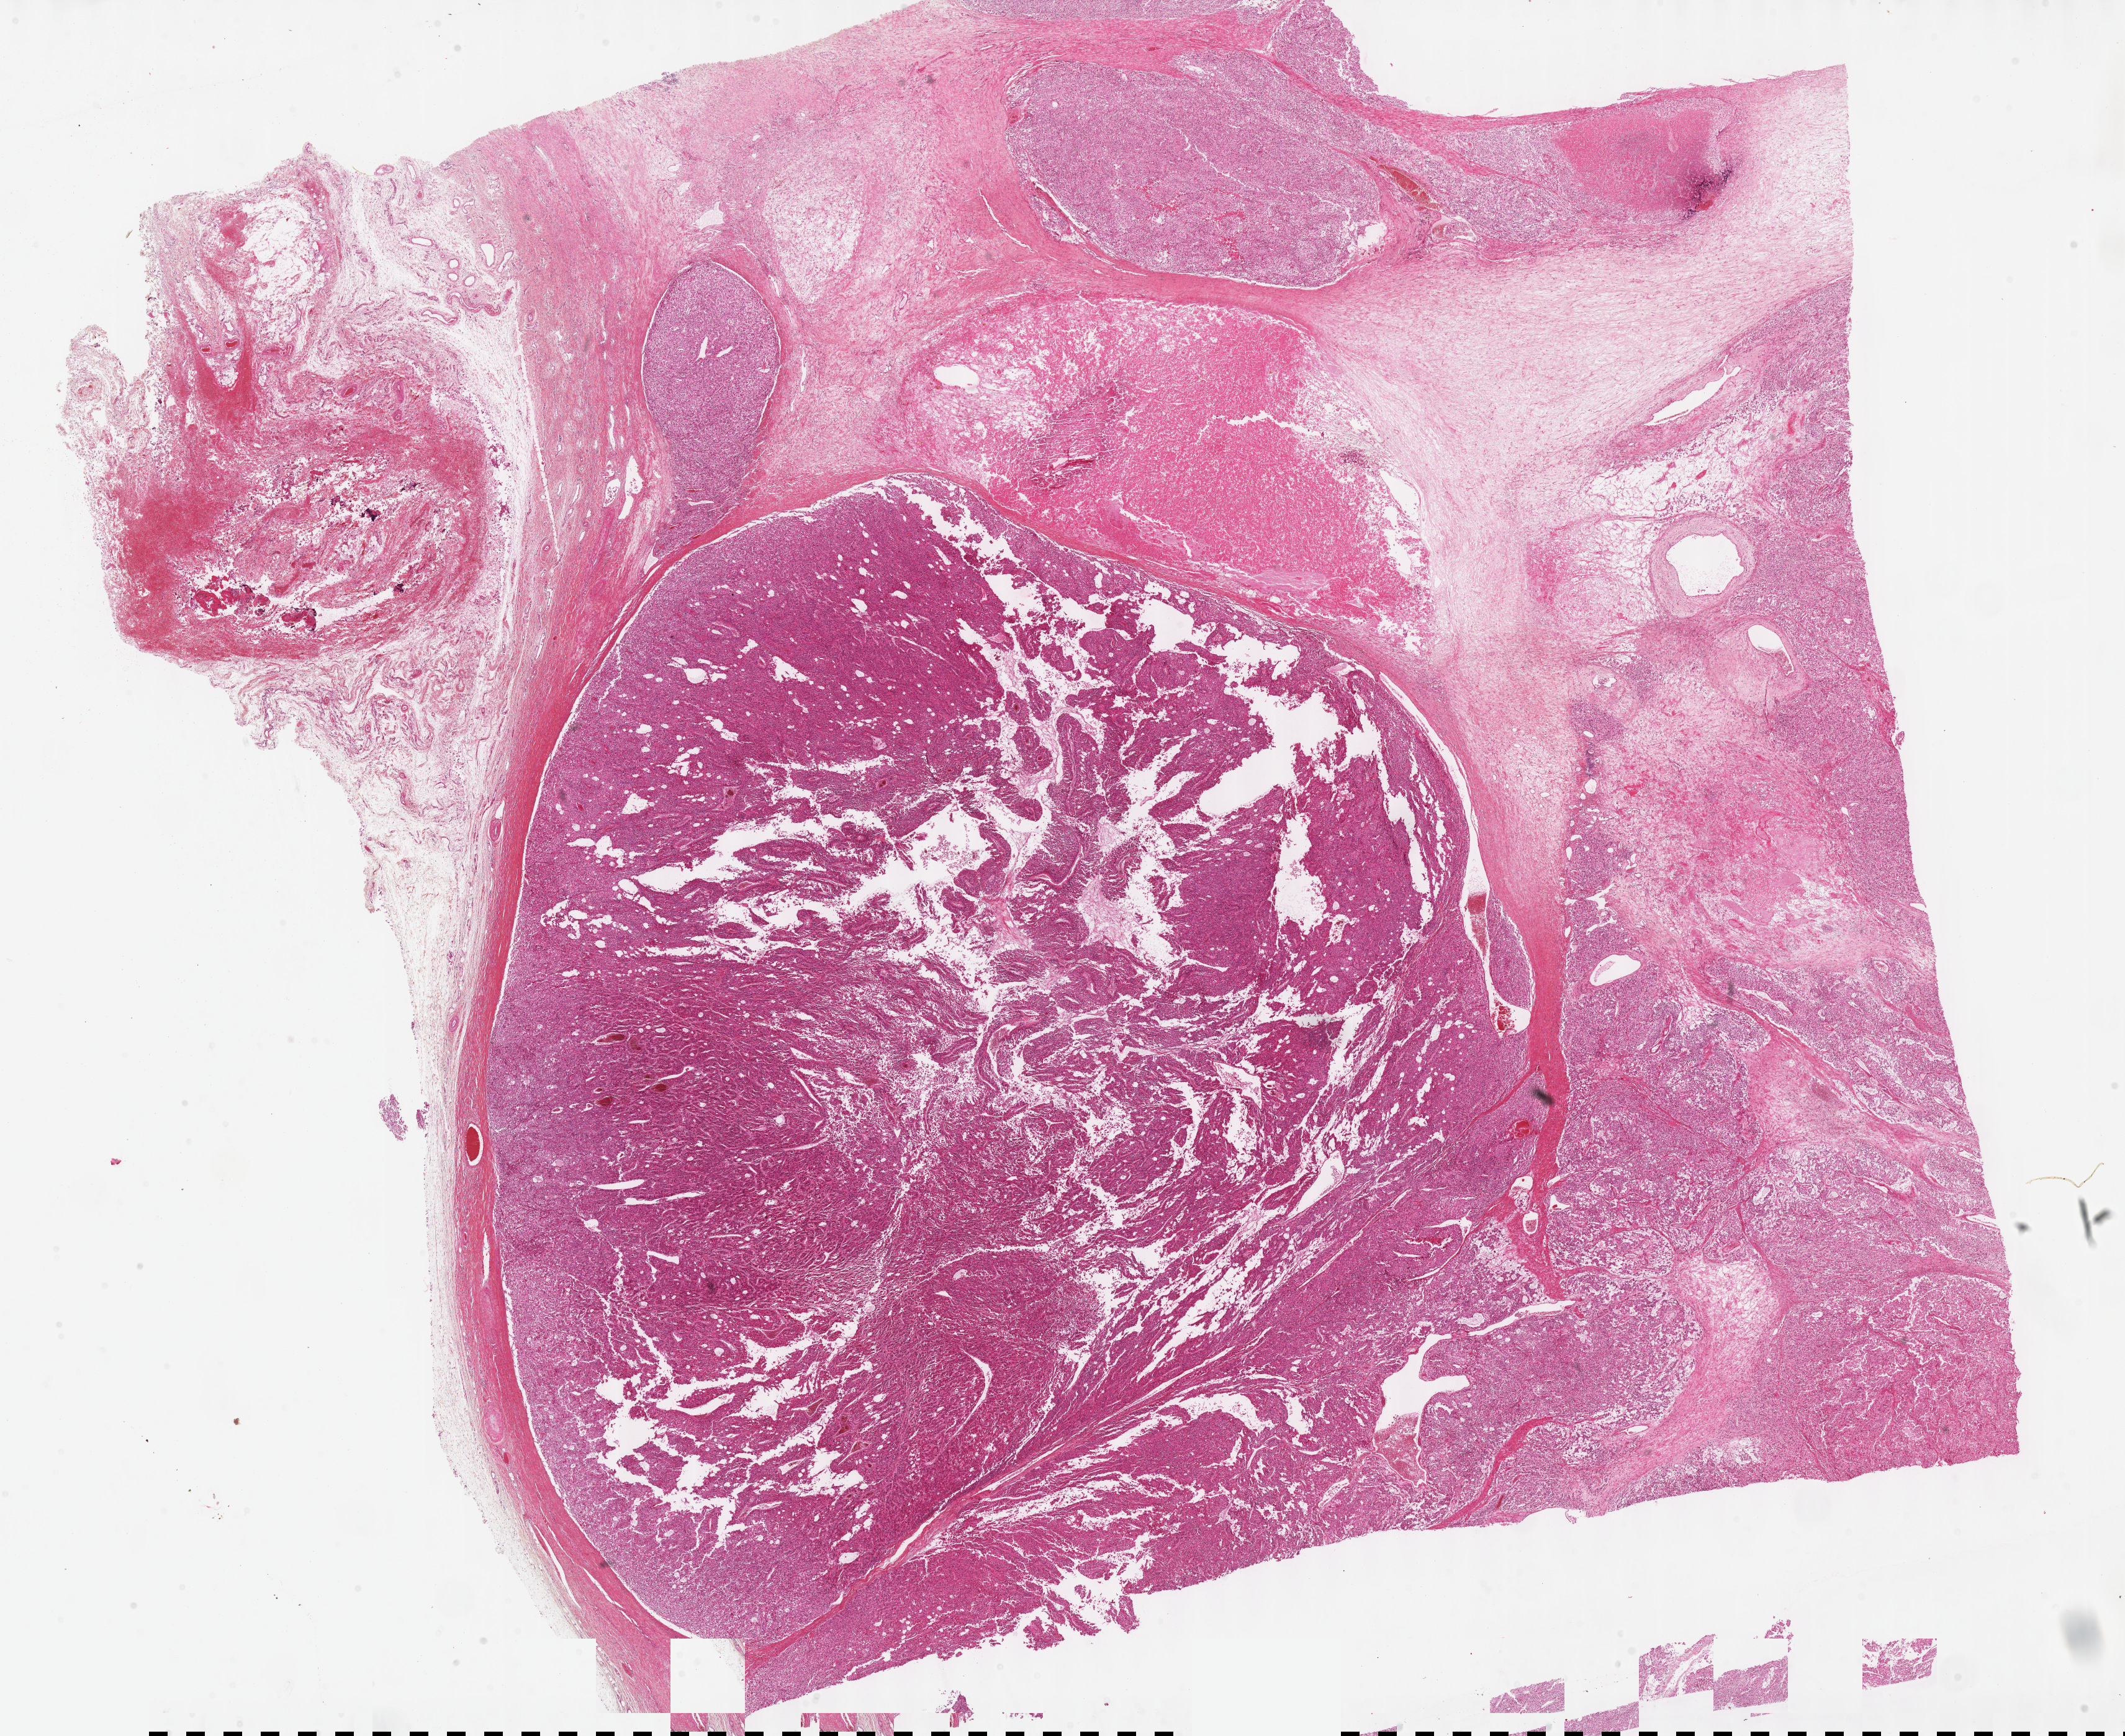
Digitized Hematoxylin and eosin (H&E) stained tissue section (whole slide), low-resolution overview of the scanned area, about 27.7 x 22.6 mm. Formalin-fixed paraffin-embedded (FFPE) diagnostic section. Sample: primary tumour, adrenal cortex. Female, age 61 years at initial diagnosis.
Lymph nodes positive (case pathology): 0 of 19 examined. Diagnosis: Adrenal cortical carcinoma. Laterality: right.